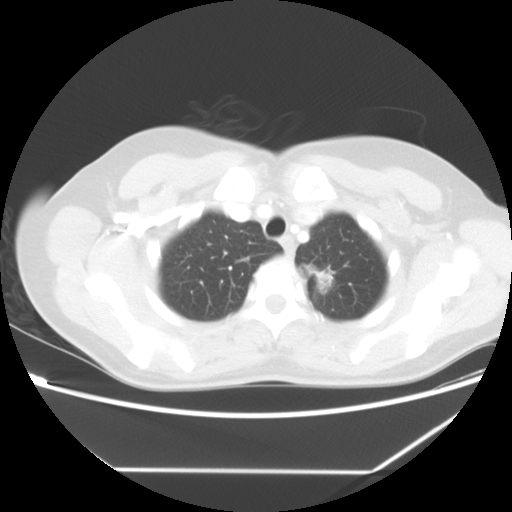
Chest CT, one axial slice; slice 50 of 60 in the series (ordered by position); 140 kVp; lung window (W 1500 / L -600 HU); 5 mm slice thickness; 512 × 512 image matrix, field of view 367 × 367 mm. Female patient, age 43 years. Case-level facts recorded for this patient, not image findings: clinical TNM (as recorded): T1c N0 M1b.
Outlined on this slice (bounding box drawn by a radiologist):
- lung tumour (recorded histology: adenocarcinoma): box from (x=313, y=263) to (x=334, y=290) px